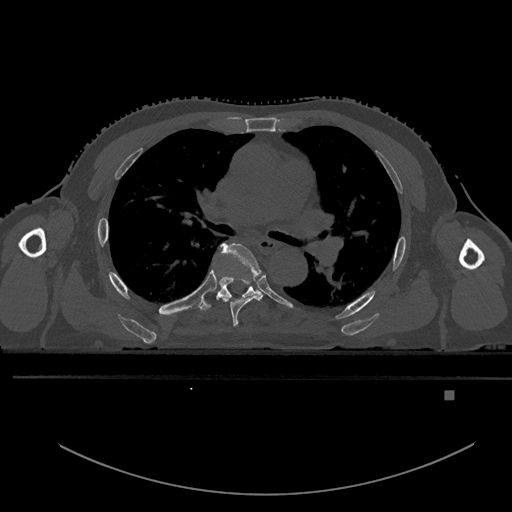
CT including the spine, one axial slice. Slice 335 of 969 in the series (ordered by position). Bone window (W 1800 / L 400 HU). 0.5 mm slice thickness. 512 × 512 image matrix. Patient: male, 82 years. From the clinical record (not read from this slice): primary cancer: prostate; vertebrae with lytic lesions (as recorded): T11, T9, T8, T2.
Structures marked on this image (semi-automatic segmentation, software-assisted and operator-edited):
- T5 vertebra: bounding box <219,243,262,327> (left, top, right, bottom; pixels)
- T6 vertebra: <197,265,261,311>